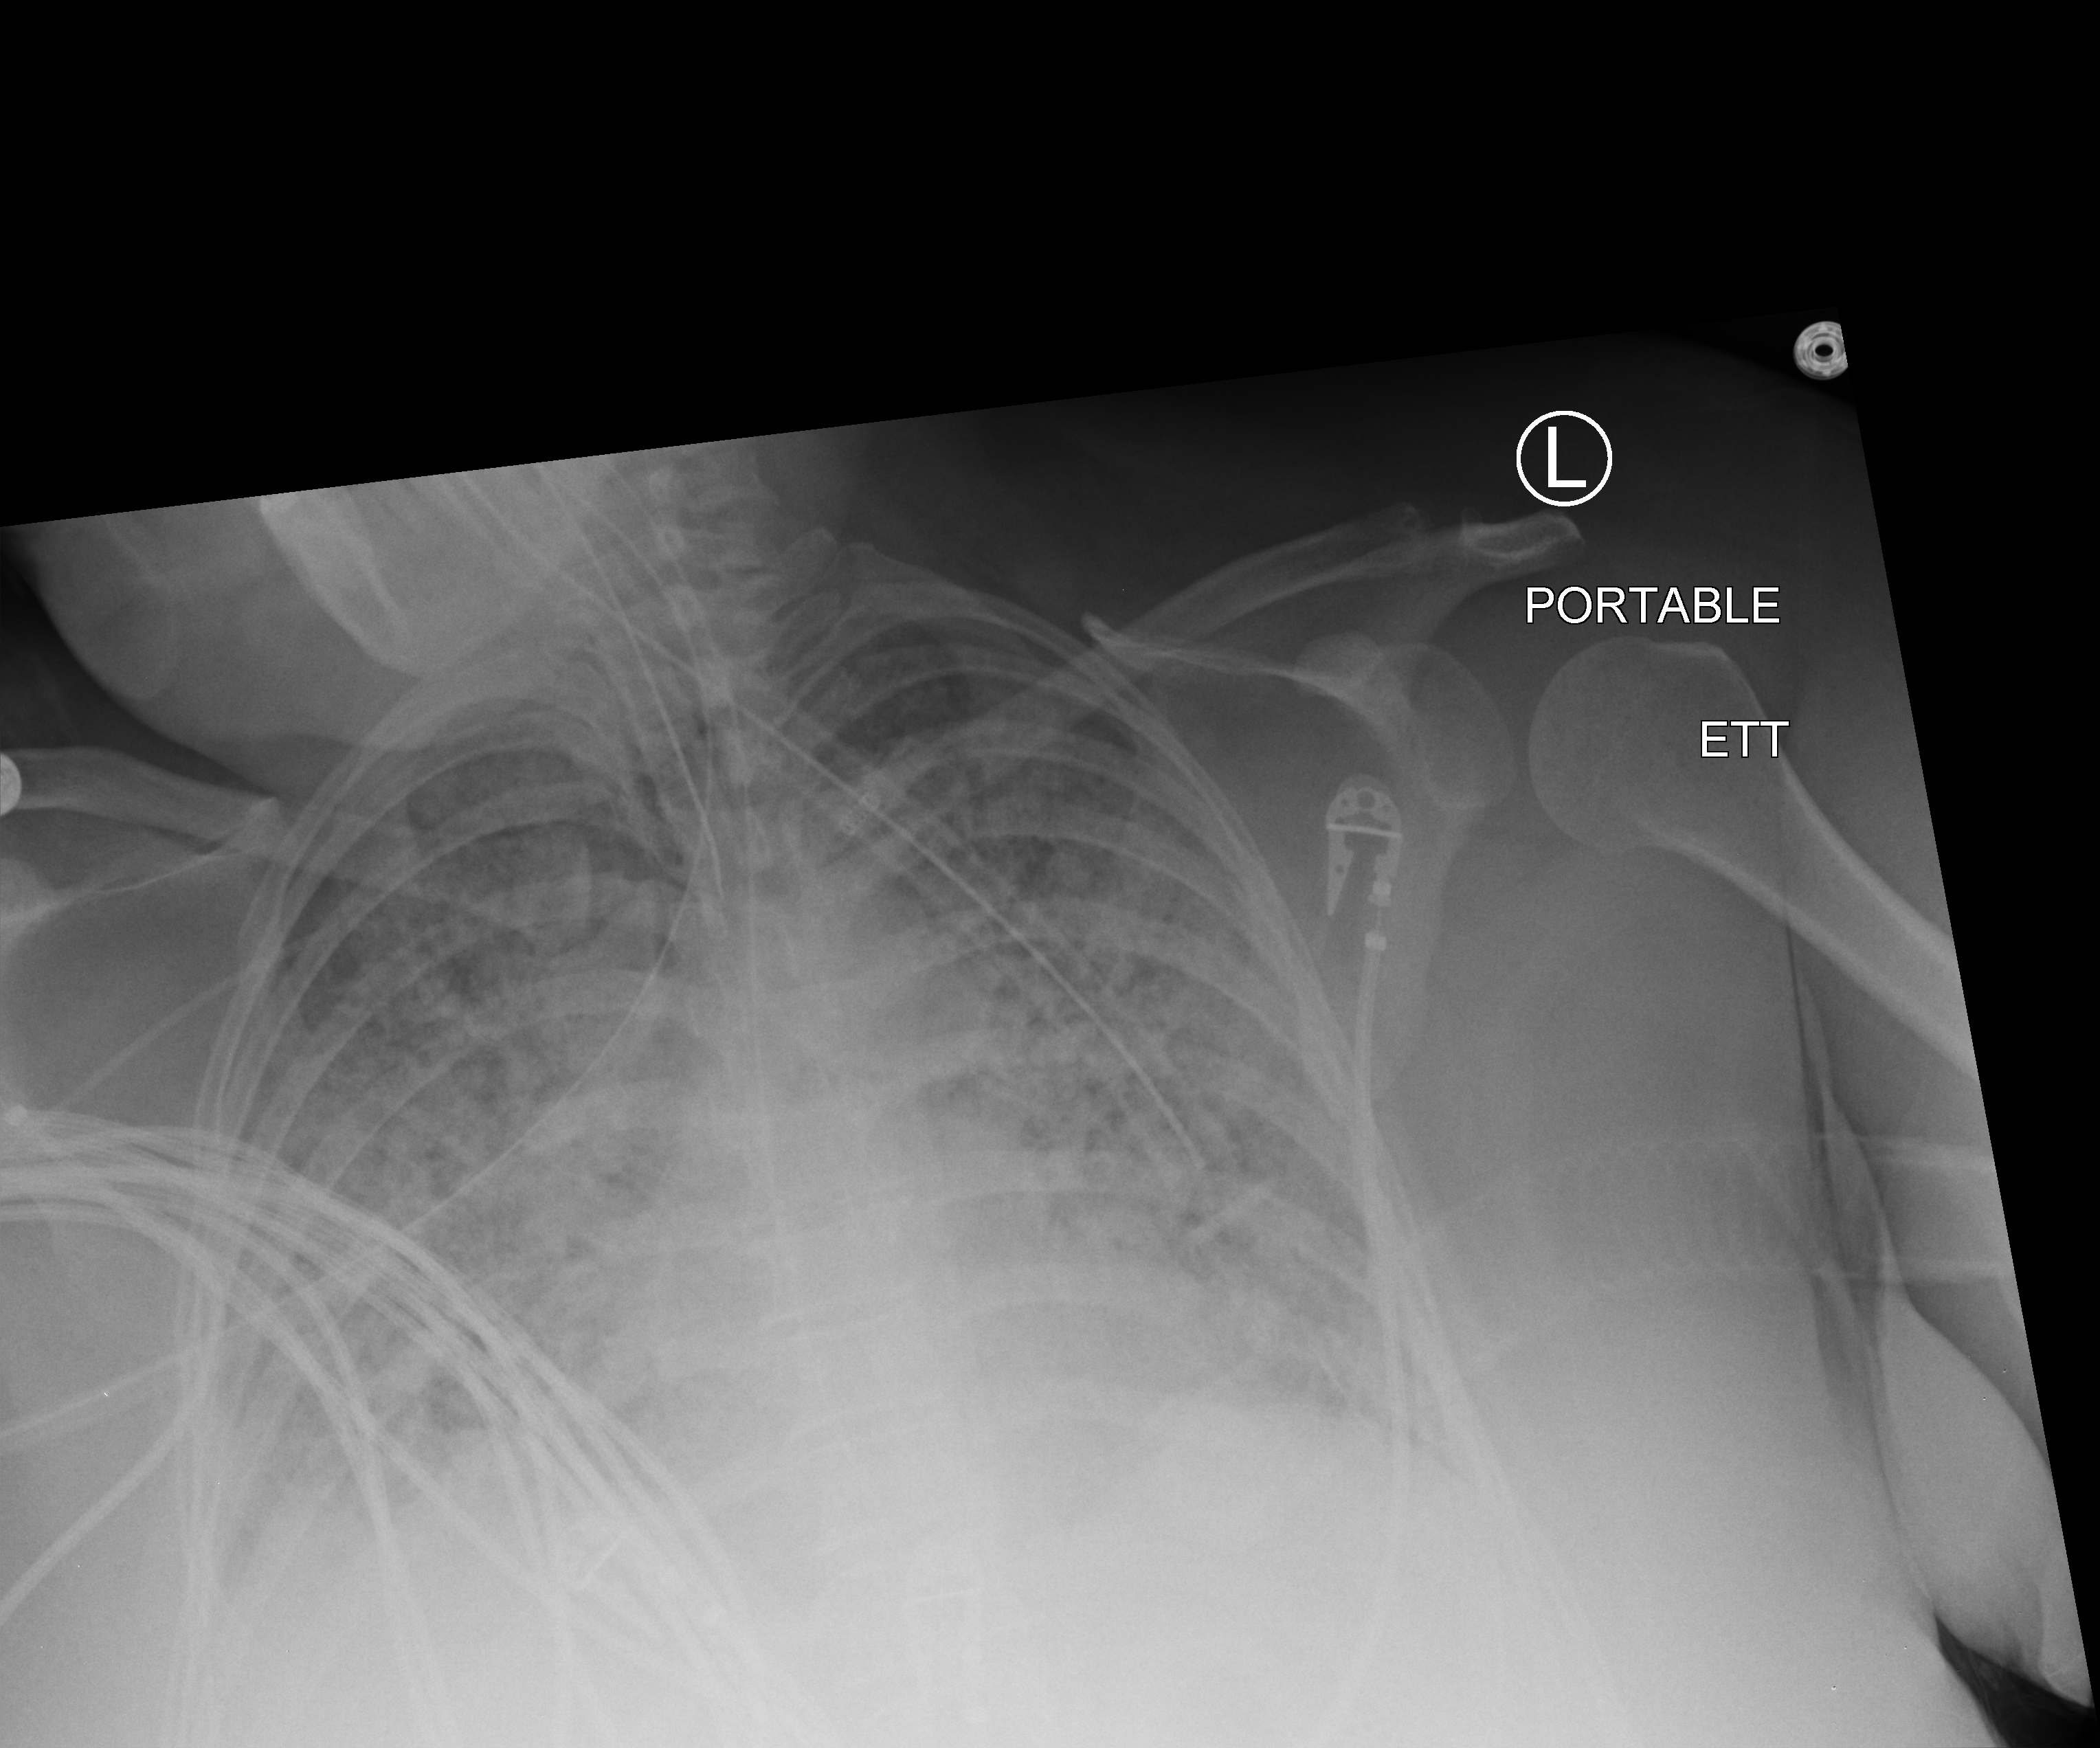
Bedside chest radiograph (computed radiography); anteroposterior (AP) projection. Patient hospitalised with COVID-19; female, aged 18–59 years.
Hospital-stay facts (about this admission, not read from this image; timing relative to this image not recorded):
- COPD (admission record): no